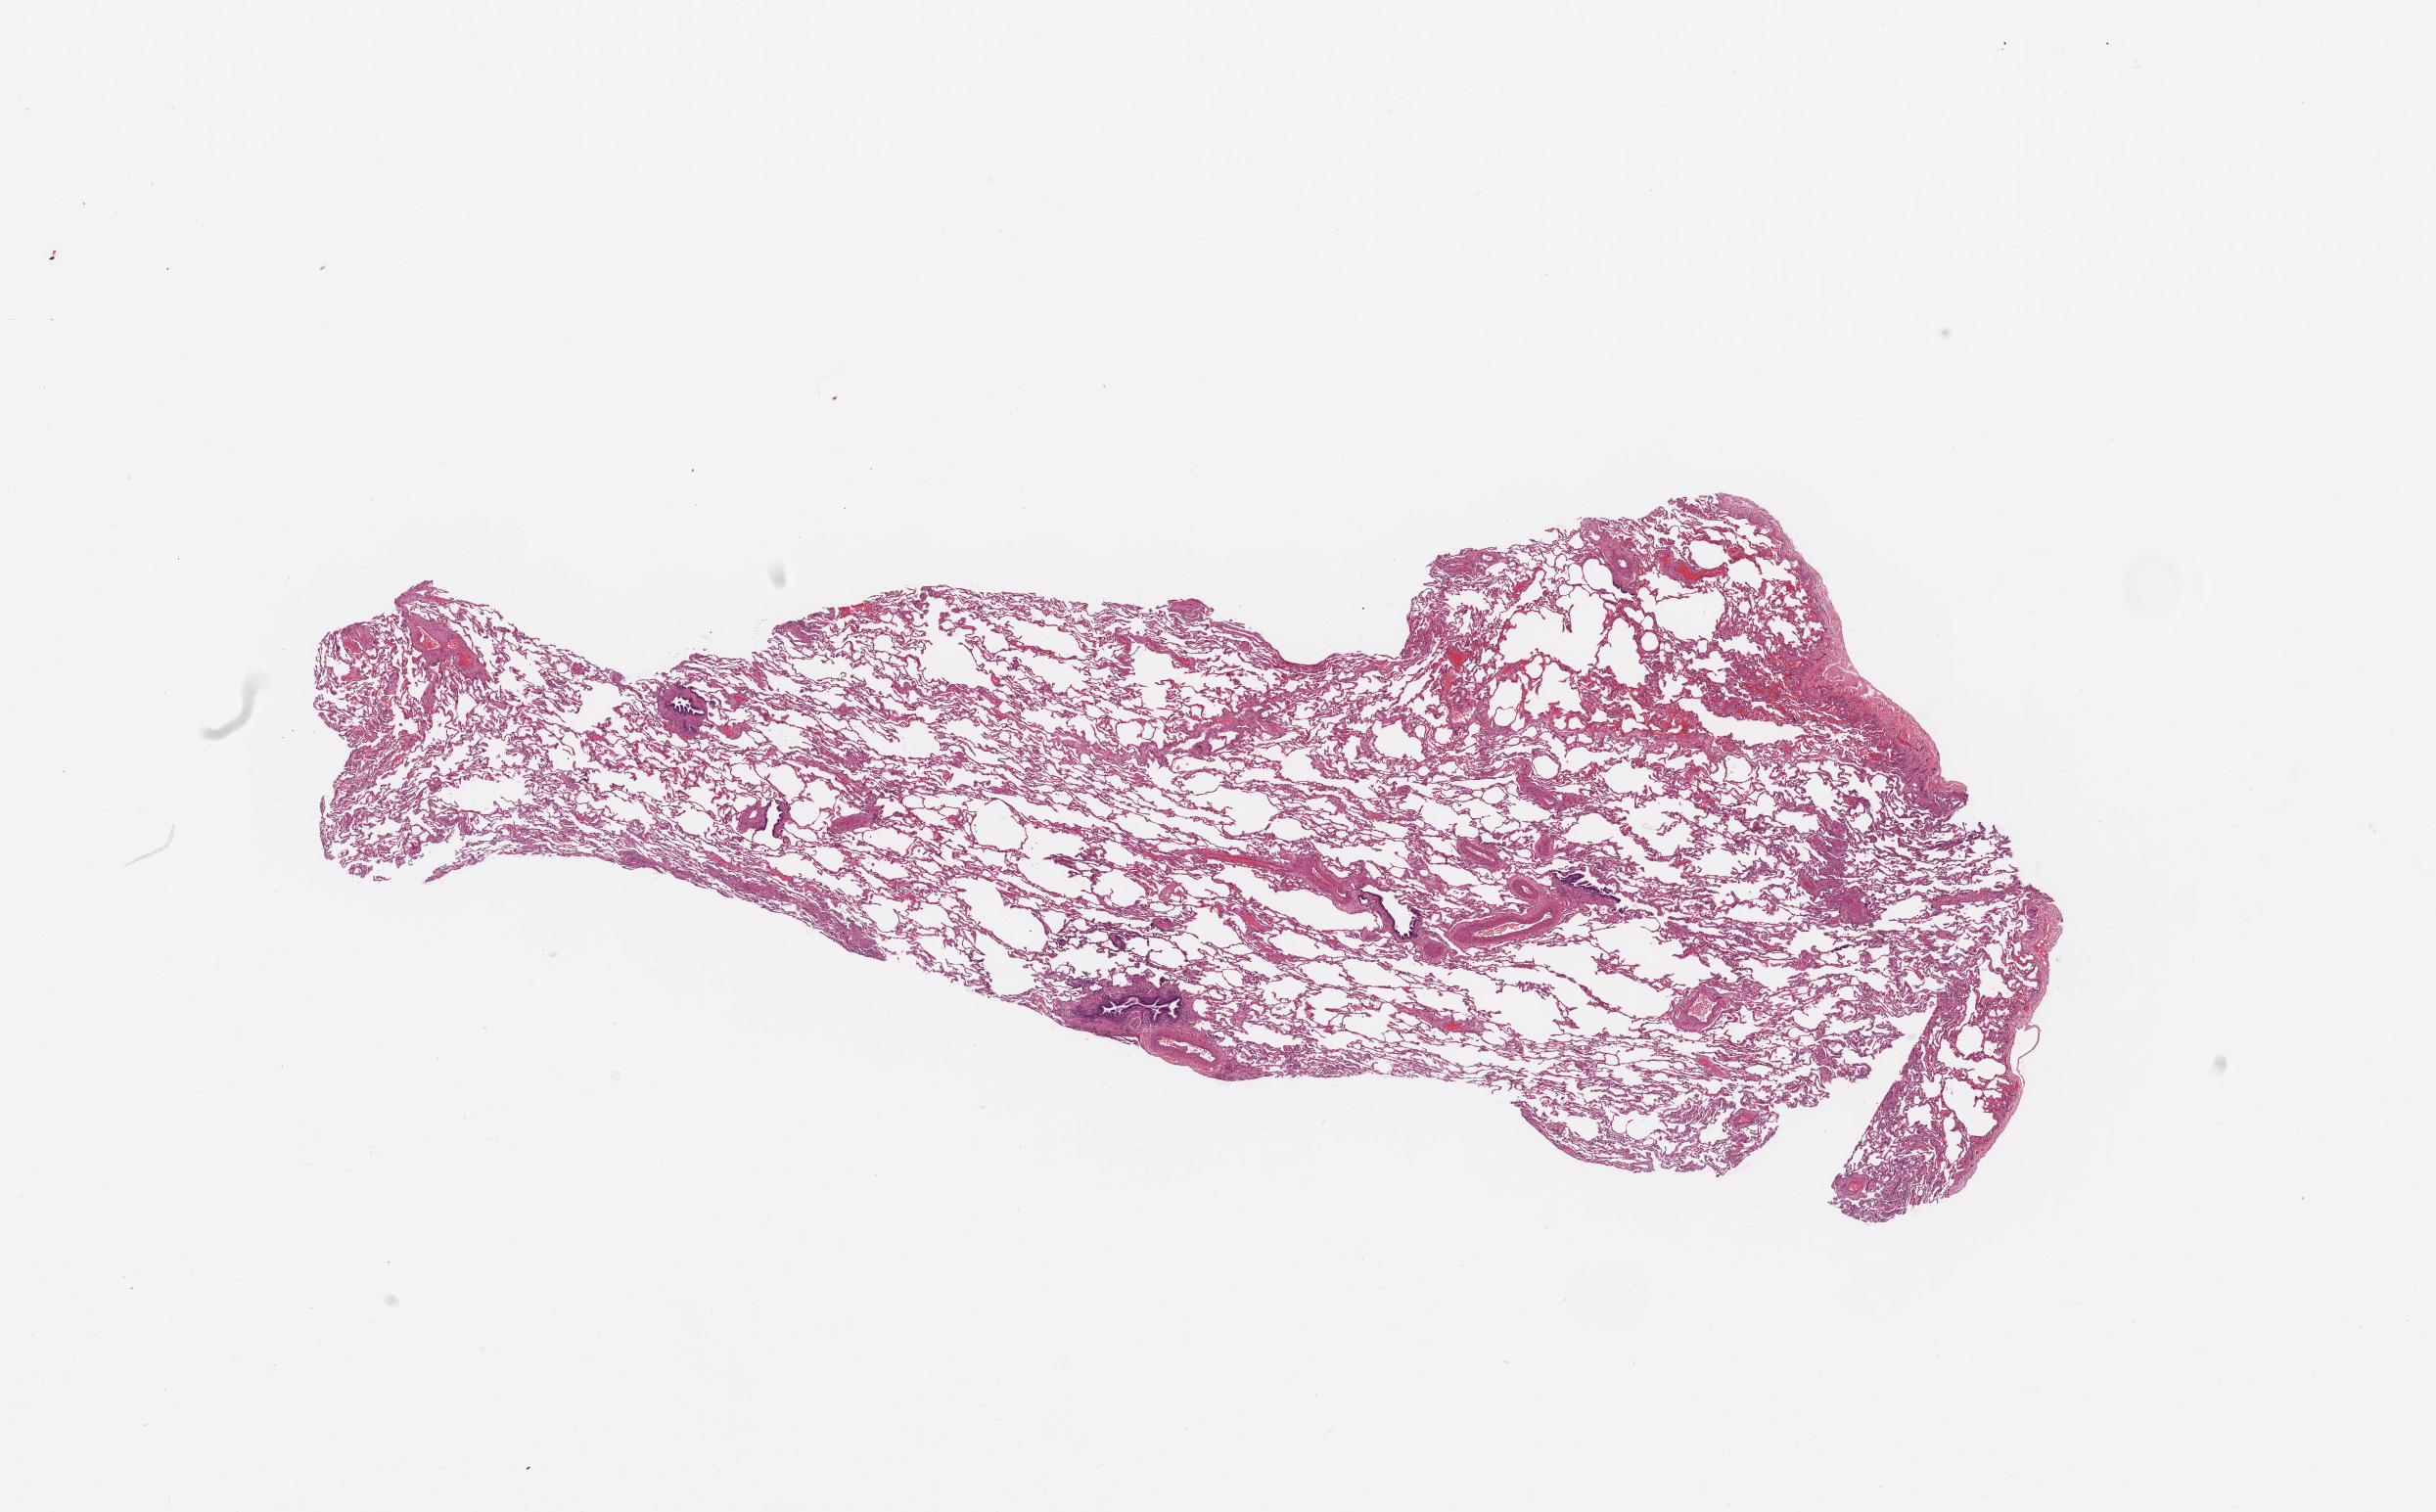
Digitized H&E-stained tissue section (whole slide) — low-resolution overview of the scanned area, about 19.7 x 12.2 mm (from a 20x scan), normal (non-tumour) tissue sample, lung. Patient: female, age 68 years.
This section: normal (non-tumour) tissue from the same patient. Patient diagnosis: Adenocarcinoma, NOS.